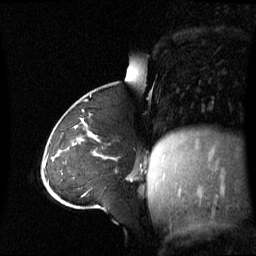
Breast MRI (dynamic contrast-enhanced), one sagittal slice. Dynamic contrast-enhanced series, image 2 of 3 at this slice position (ordered by acquisition). 1.5 T. TE 4.2 ms, TR 8.4 ms. 256 × 256 image matrix, field of view 270 × 270 mm. Patient: female, 43 years. Case-level facts recorded for this patient, not image findings: setting: breast cancer imaged before/during neoadjuvant chemotherapy; receptor status: triple-negative.
Outlined on this slice (semi-automatically segmented with operator editing):
- analysis volume of interest (the breast-tissue region the enhancement analysis was run in; not a lesion): bounding box (x1, y1, x2, y2) in pixels: (55, 124, 136, 173)
- tumour enhancement mask (voxels above the 70 % enhancement threshold inside the analysis volume of interest): (72, 126, 77, 146)